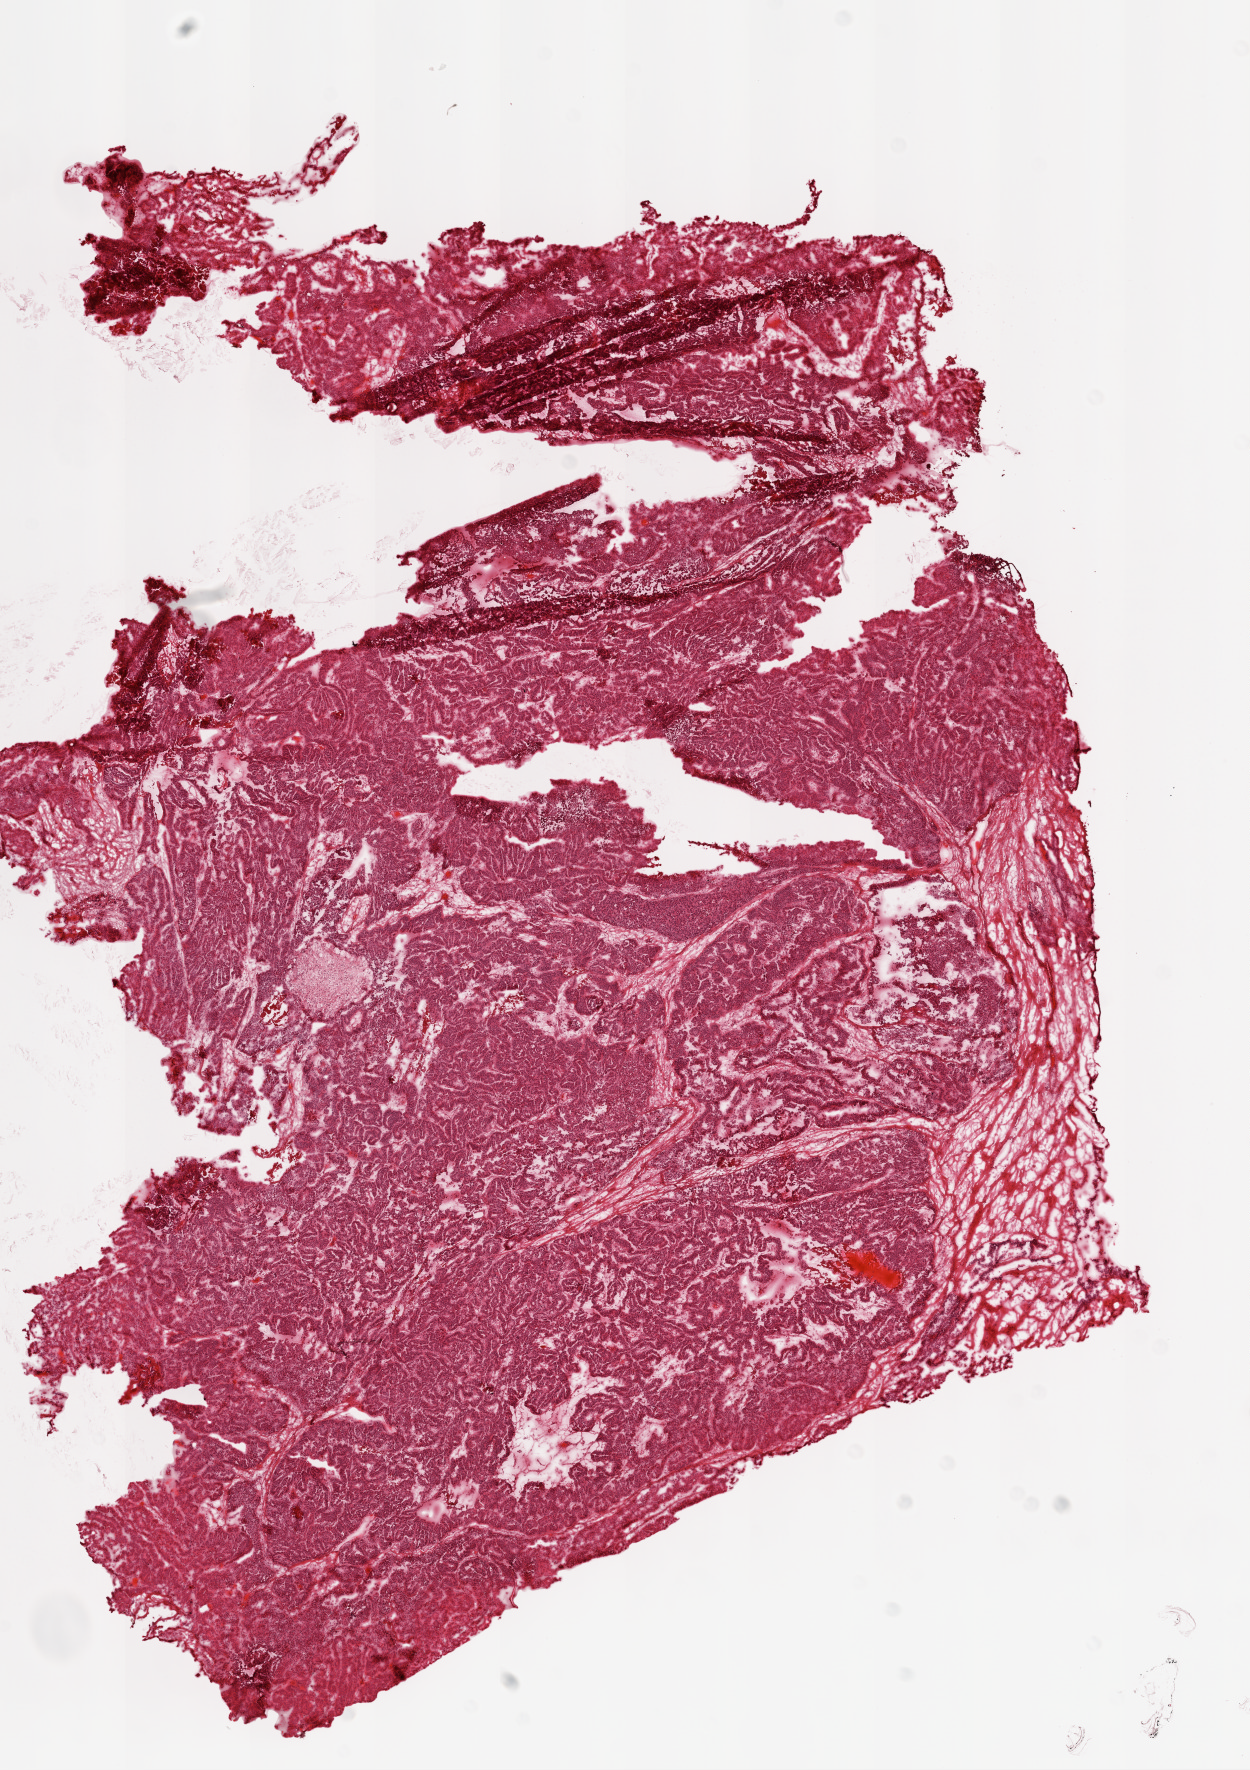
Whole-slide histology image, H&E-stained — low-resolution overview of the scanned area, about 10.0 x 14.2 mm (acquisition: 20x scan); frozen section; ovary, primary tumour sample. Female, age 49 years at initial diagnosis. Histologic grade: G3 (poorly differentiated). Pathologist review of this section (percent, as recorded): tumour cells 90%, tumour nuclei 90%, normal cells 0%, stromal cells 8%, necrosis 2%.
Laterality: bilateral. Histologic diagnosis: Serous cystadenocarcinoma, NOS. FIGO stage: IIIC.